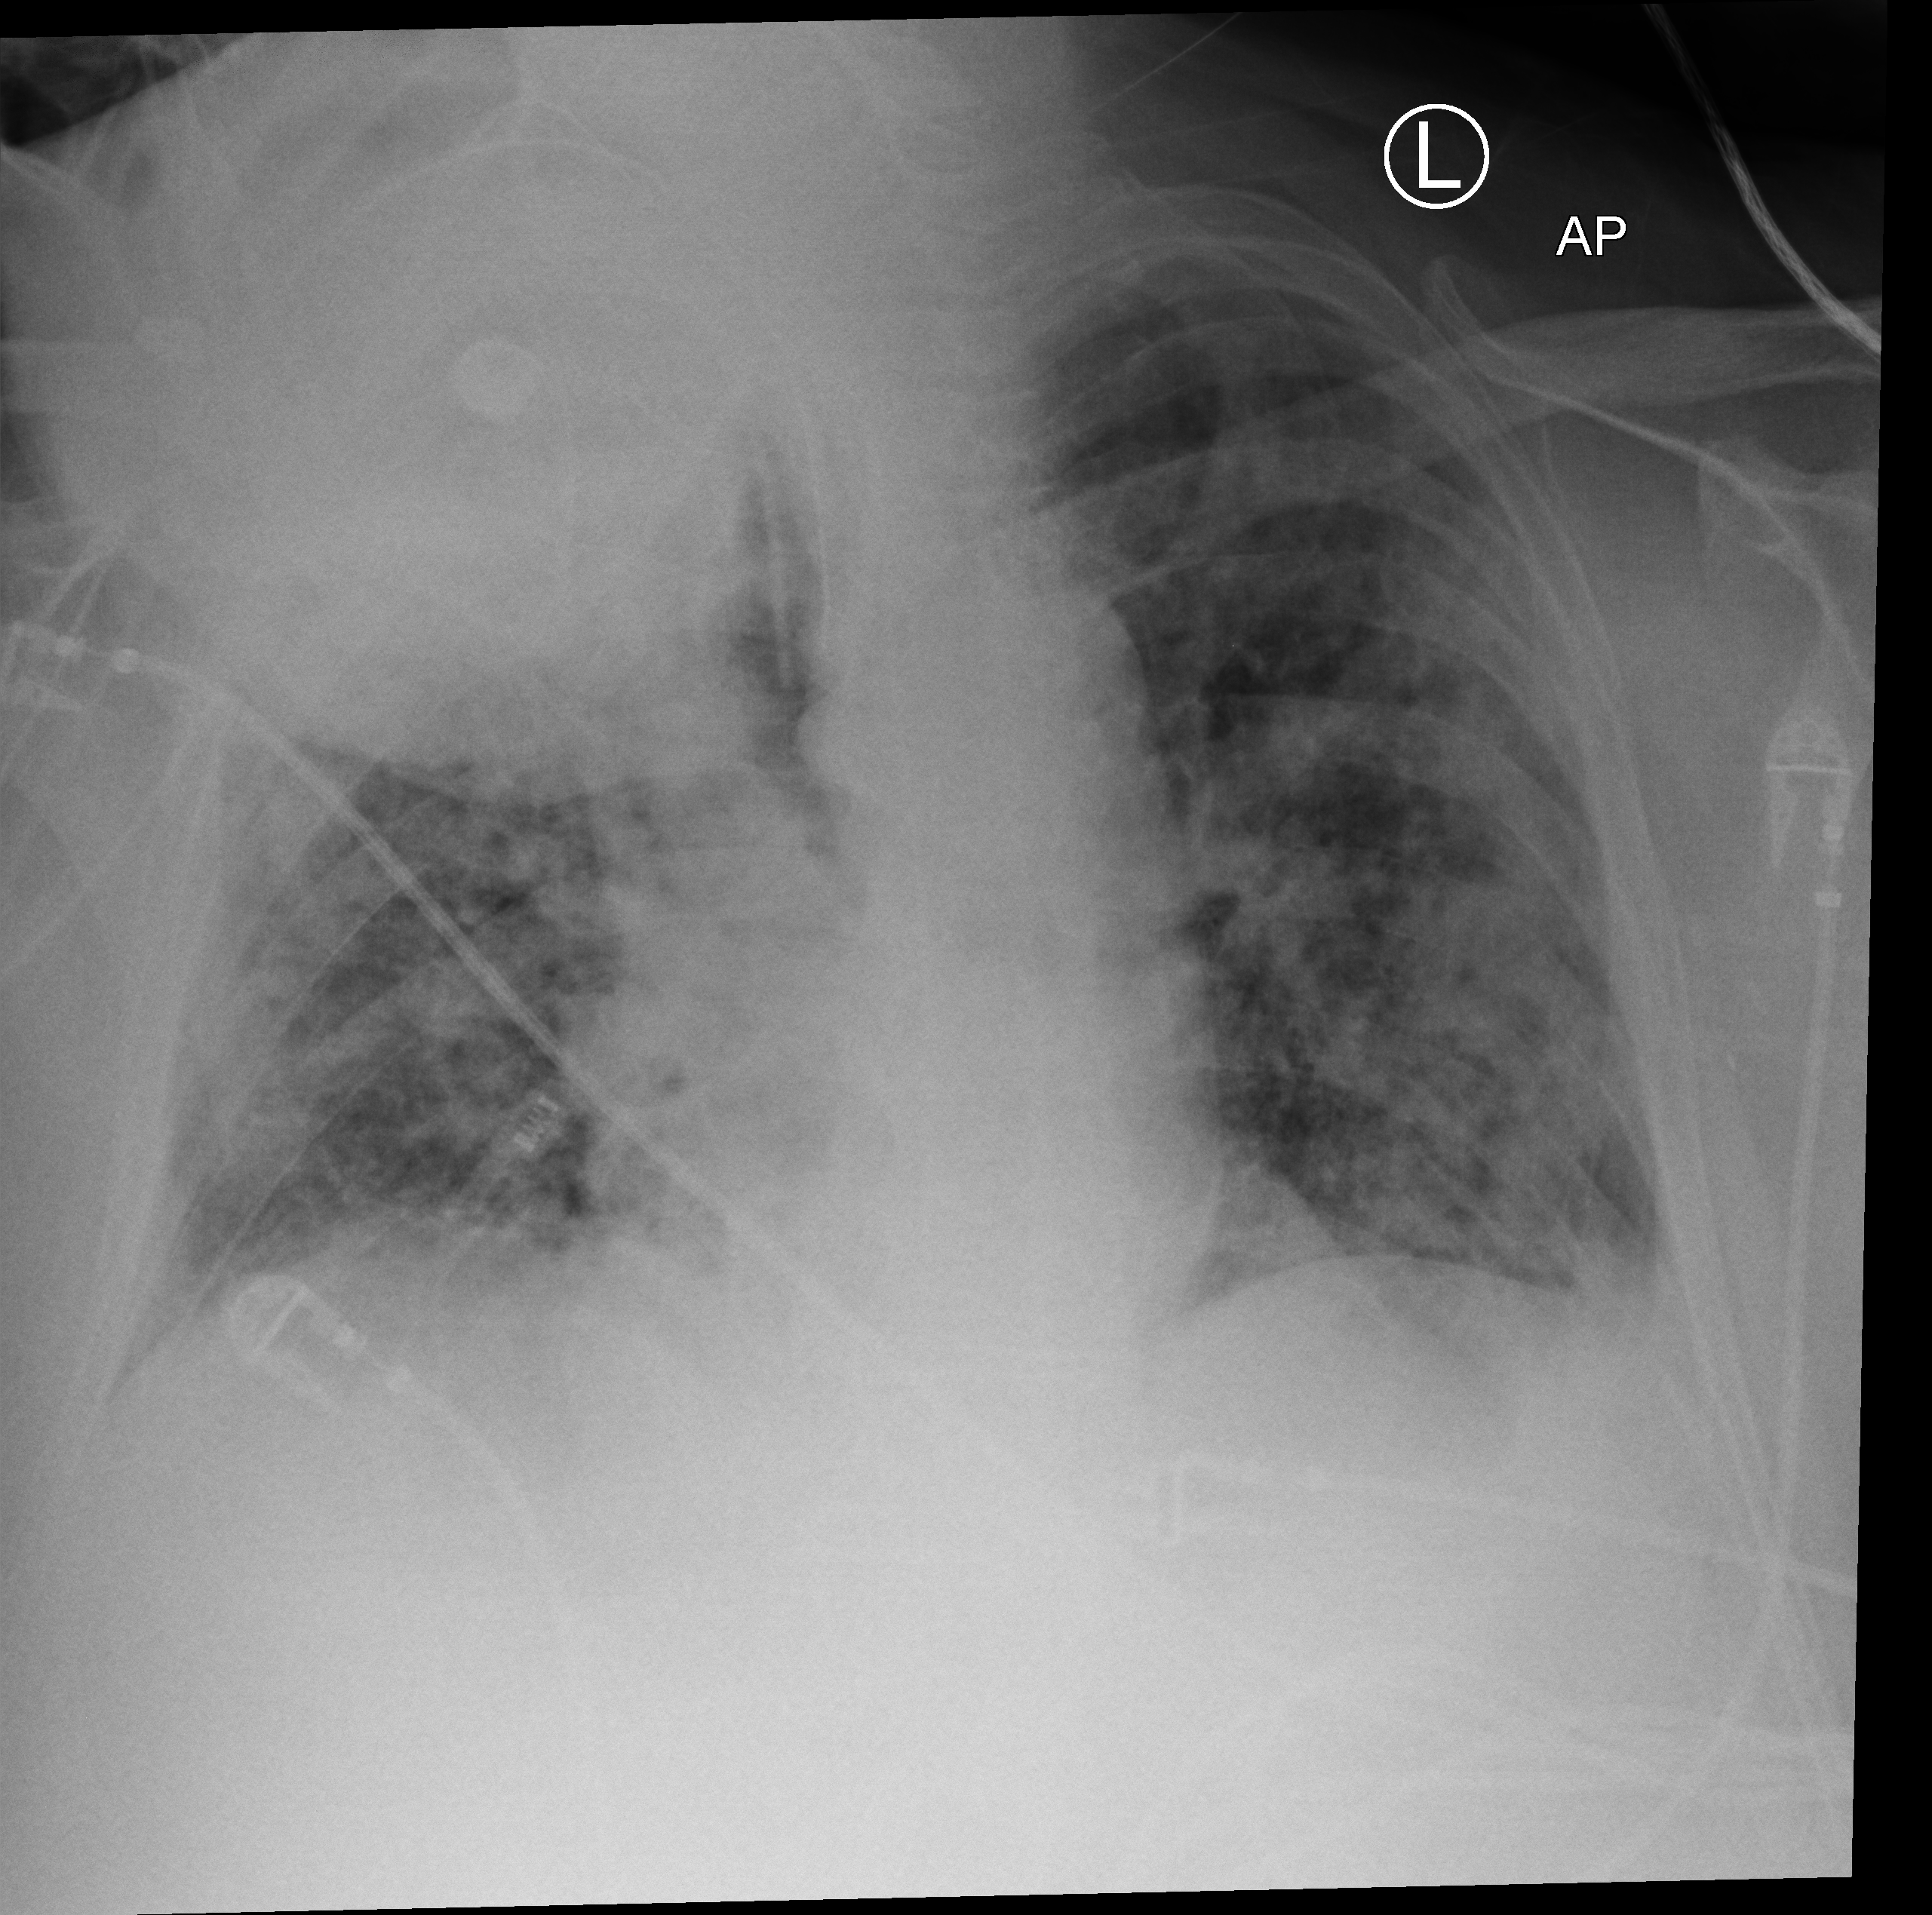
Portable chest radiograph; anteroposterior (AP) projection. Male patient hospitalised with COVID-19, age 60–74 years.
From the hospital-stay record, not from the radiograph (when in the stay this image was taken is not recorded): admitted to intensive care during this hospital stay: yes; chronic kidney disease (admission record): no; mechanically ventilated during this hospital stay: yes.